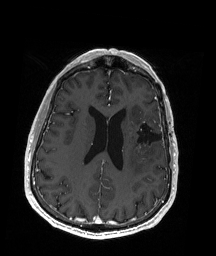
Brain MRI from a brain-tumour surgery series, one axial slice; slice 76 of 192 in the series (ordered by position); T1-weighted post-contrast; 1 mm slice thickness; 216 × 256 image matrix, field of view 211 × 250 mm. Case-level facts recorded for this patient, not image findings: histopathology: Oligodendroglioma; WHO grade: 2; IDH mutation: yes; tumour location: Left Insular.
Annotated regions visible in this slice (expert manual segmentation):
- previous resection cavity: box from (x=132, y=121) to (x=163, y=148) px
- tumour: (x=138, y=122)–(x=151, y=152)